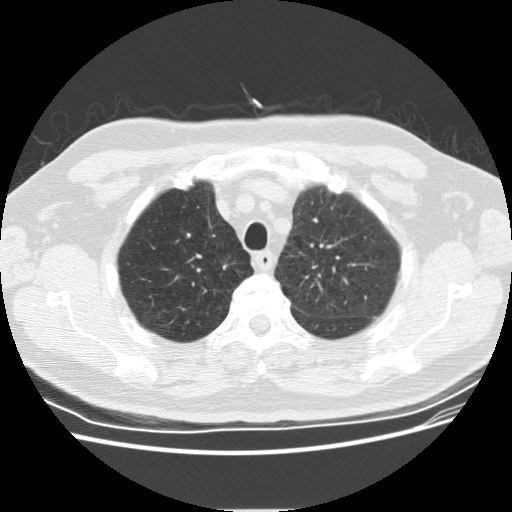
Chest CT (low-dose screening protocol), one axial image; second screening round (one year after baseline); lung window (W 1500 / L -600 HU); 2.5 mm slice thickness; standard (soft-tissue) reconstruction kernel (STANDARD); slice 120 of 152 in the series. Male participant, aged 69 years at enrolment.
• Expert reader's lesion annotation, bounding box (x1, y1, x2, y2) in pixels: (210, 255, 242, 283).
• Screening reader's record for this exam (one nodule recorded; not confirmed to be the boxed lesion): non-calcified nodule or mass ≥4 mm, right lower lobe, 4 × 4 mm, smooth margins, soft tissue attenuation, pre-existing on the prior screen: yes; interval growth: no.
• Participant outcome: lung cancer diagnosed 435 days after this screen (after the third annual screen) — squamous cell carcinoma, NOS, right upper lobe, moderately differentiated (G2), stage IA (AJCC 6th edition), 9 mm at pathology.